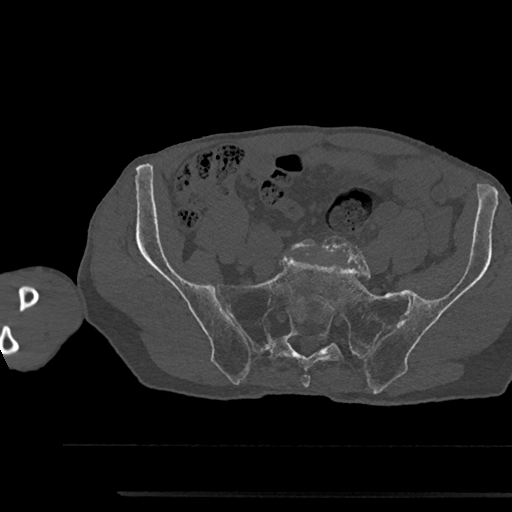
CT including the spine, one axial slice; slice 276 of 797 in the series (ordered by position); bone window (W 1800 / L 400 HU); 0.5 mm slice thickness; 512 × 512 image matrix, field of view 367 × 367 mm. Male patient, age 79 years. Case-level facts recorded for this patient, not image findings: primary cancer: prostate.
Outlined on this slice (semi-automatic segmentation, software-assisted and operator-edited):
- L5 vertebra: bounding box <291,238,316,250> (left, top, right, bottom; pixels)